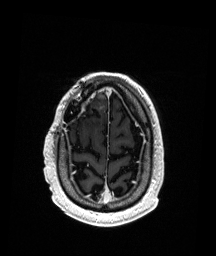
Brain MRI from a brain-tumour surgery series, one axial slice; slice 38 of 192 in the series (ordered by position); T1-weighted post-contrast; 1 mm slice thickness; 216 × 256 image matrix, field of view 211 × 250 mm. Case-level facts recorded for this patient, not image findings: histopathology: Astrocytoma; WHO grade: 3; IDH mutation: yes.
Outlined on this slice (outlined manually by an expert reader):
- previous resection cavity: bounding box [x1, y1, x2, y2] px = [81, 104, 101, 118]
- tumour: [94, 89, 105, 98]